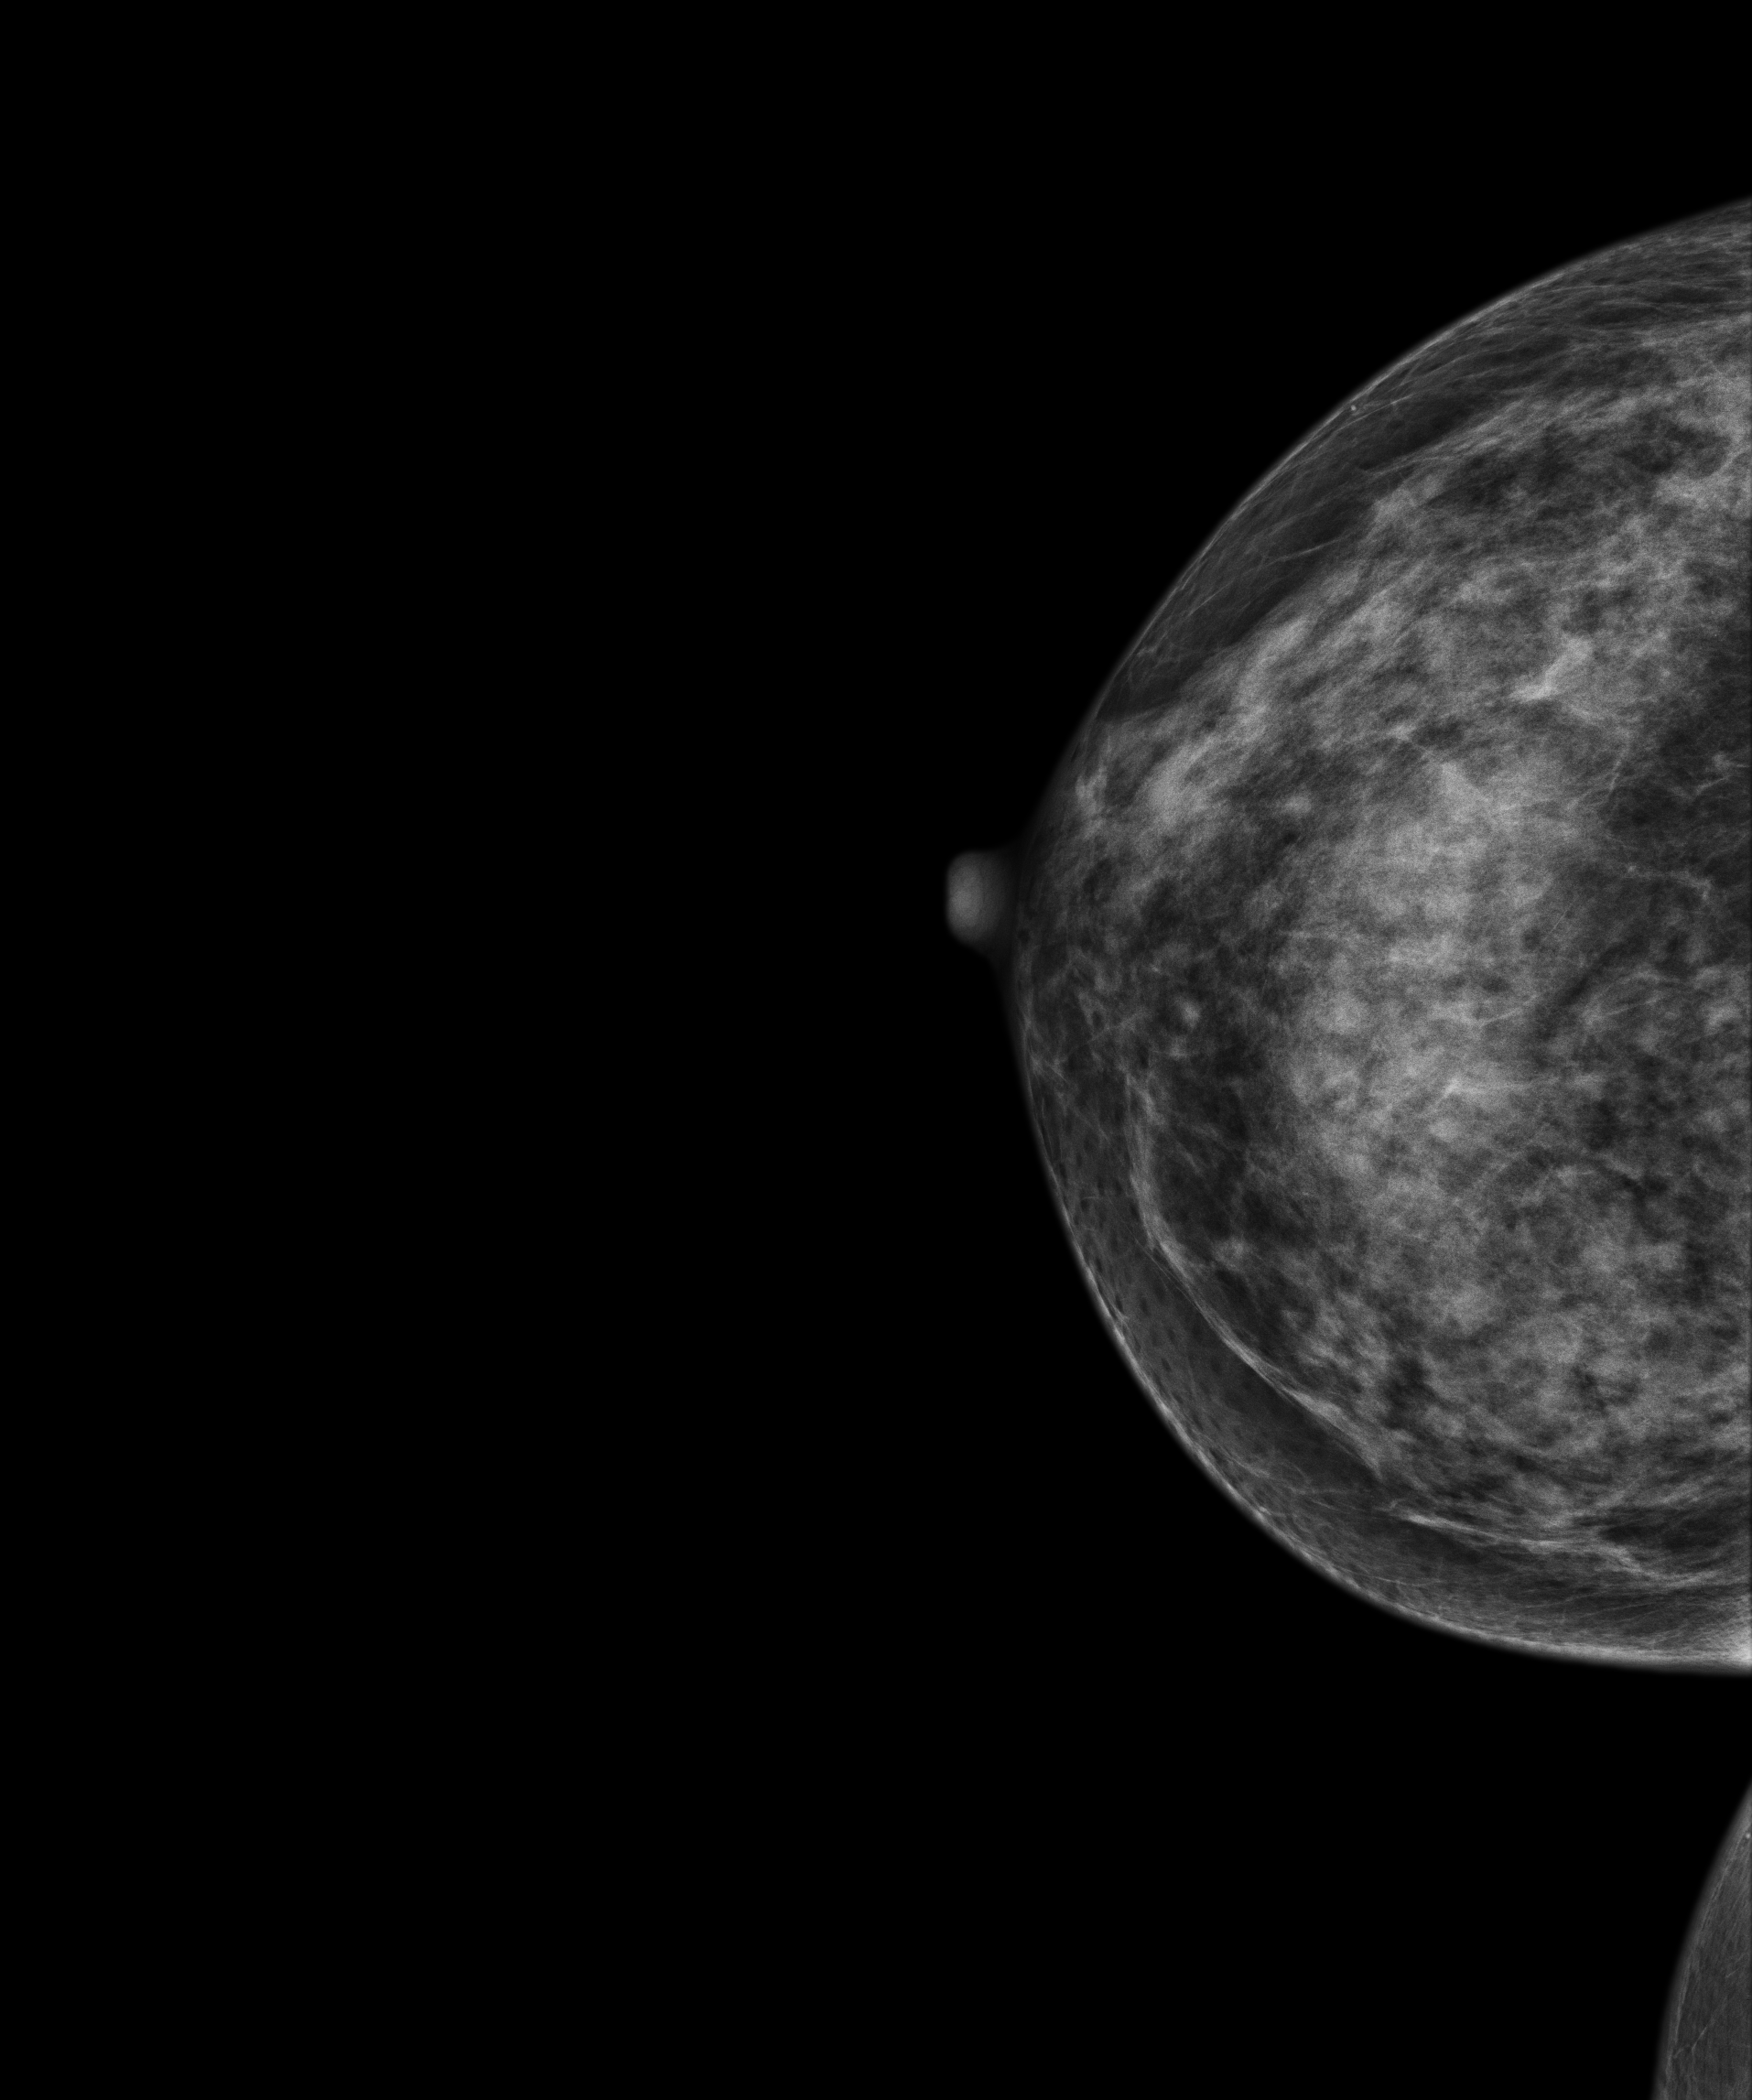
Digital mammogram (FFDM), right breast, CC view, screening examination, compressed breast thickness 47 mm. Female patient, age 60 years.
Breast density at the screening exam (both breasts): extremely dense (BI-RADS density category d). Final BI-RADS category for the screening round (tomosynthesis exam, both breasts): category 1. Recall: no recall after this screen.